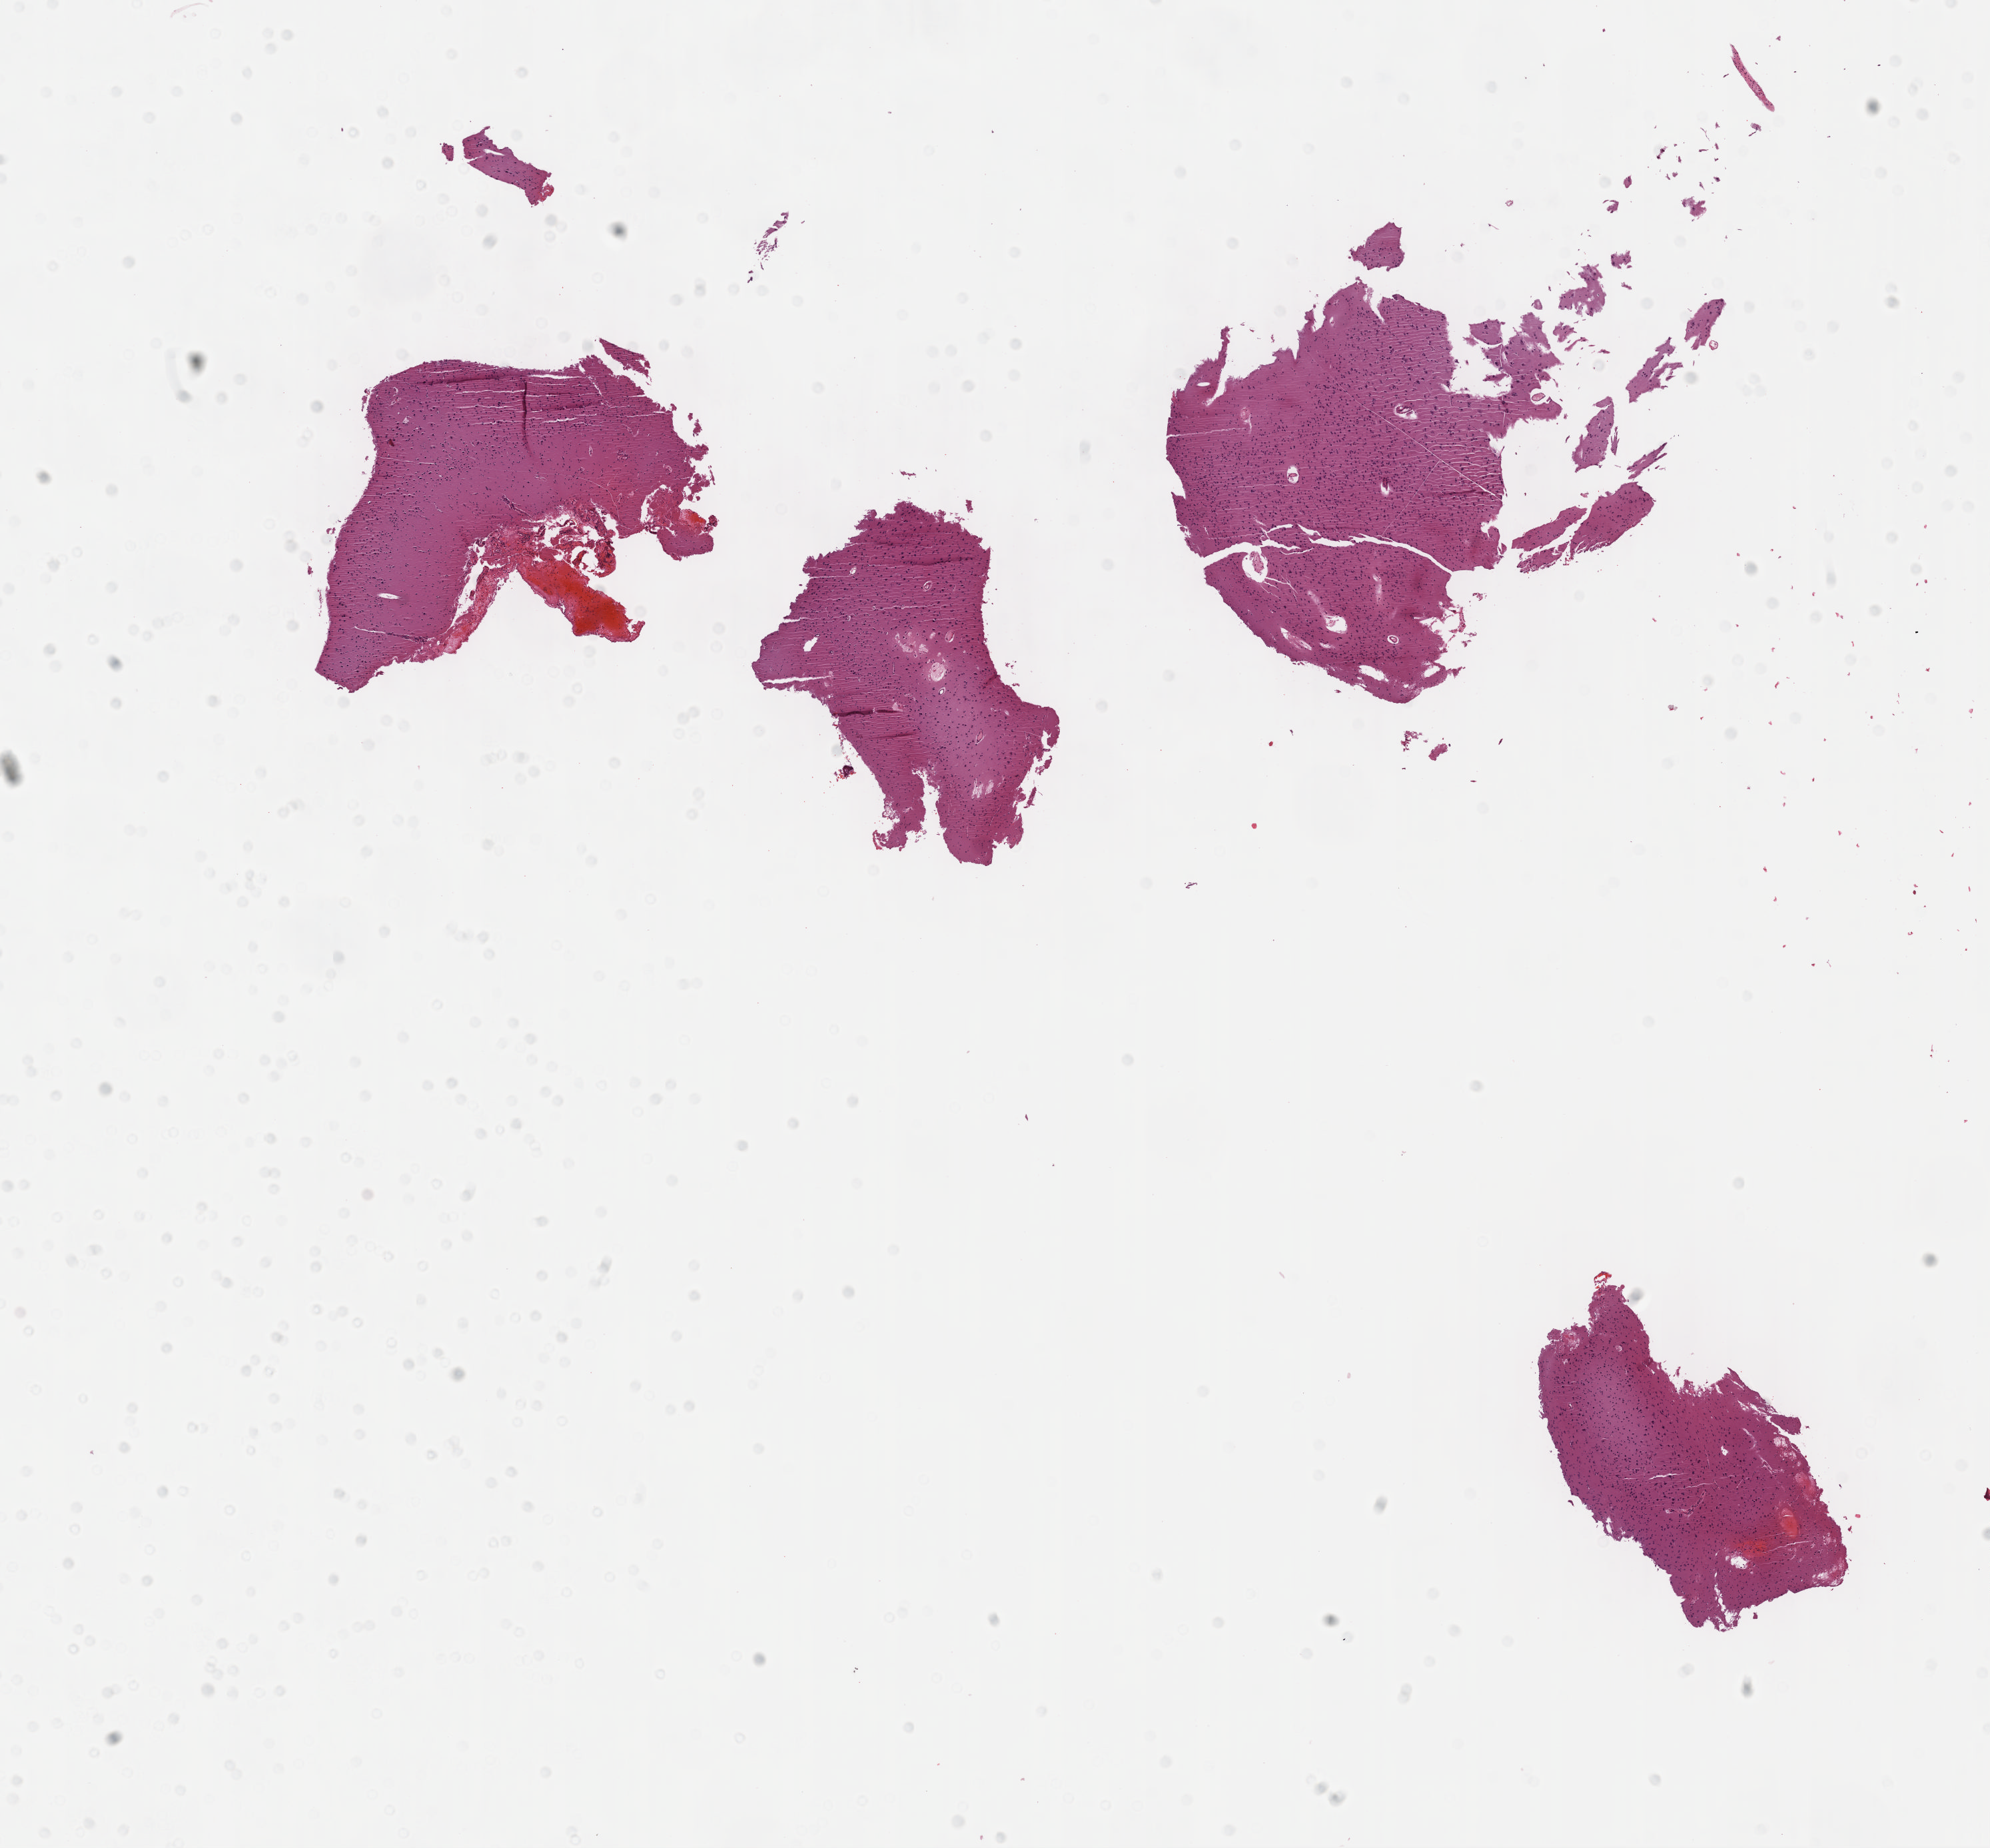
Hematoxylin and eosin (H&E) stained whole-slide image — shown as a low-resolution overview of the whole scanned area (about 12.1 x 11.2 mm); formalin-fixed paraffin-embedded (FFPE) diagnostic section; sample: primary tumour, brain. Female, age 18 years at initial diagnosis. Histologic grade: G2 (moderately differentiated).
Pathologic diagnosis: Mixed glioma.